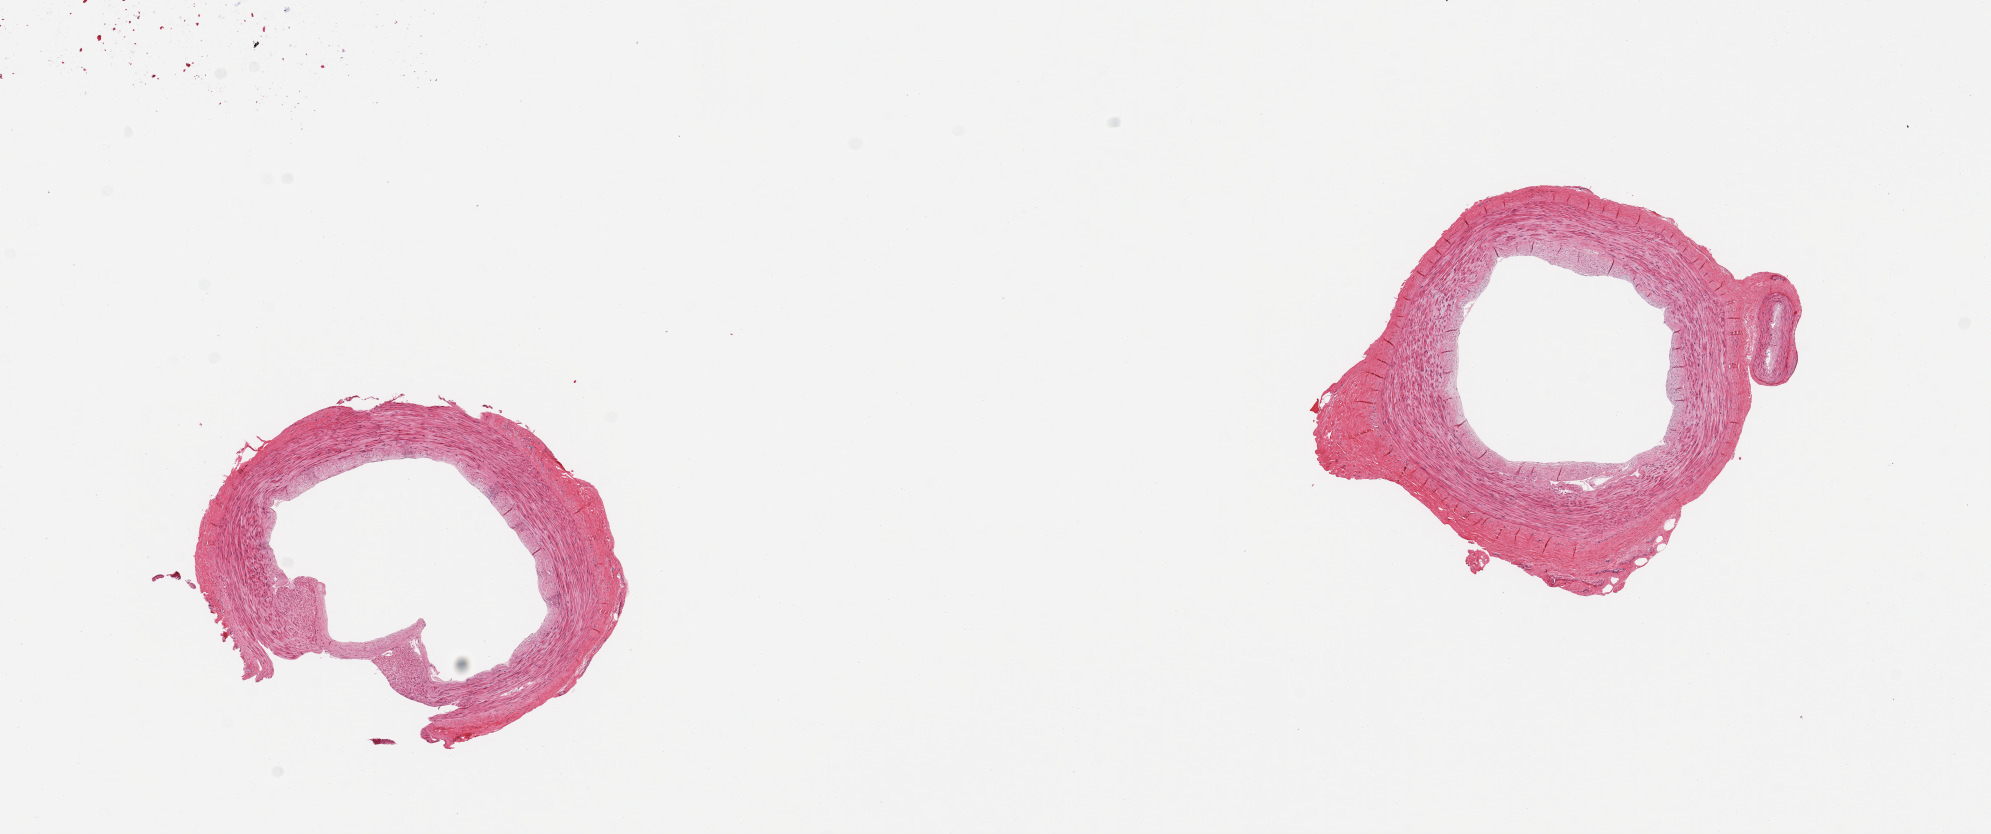
Haematoxylin and eosin whole-slide image, brightfield — a low-resolution overview of the entire scanned area, about 15.8 x 6.6 mm (from a 20x scan); PAXgene-fixed, paraffin-embedded tissue; target tissue: tibial artery; tissue donor sample. Male donor.
• pathologist's review note for this sample: 2 pieces; minimal intimal thickening